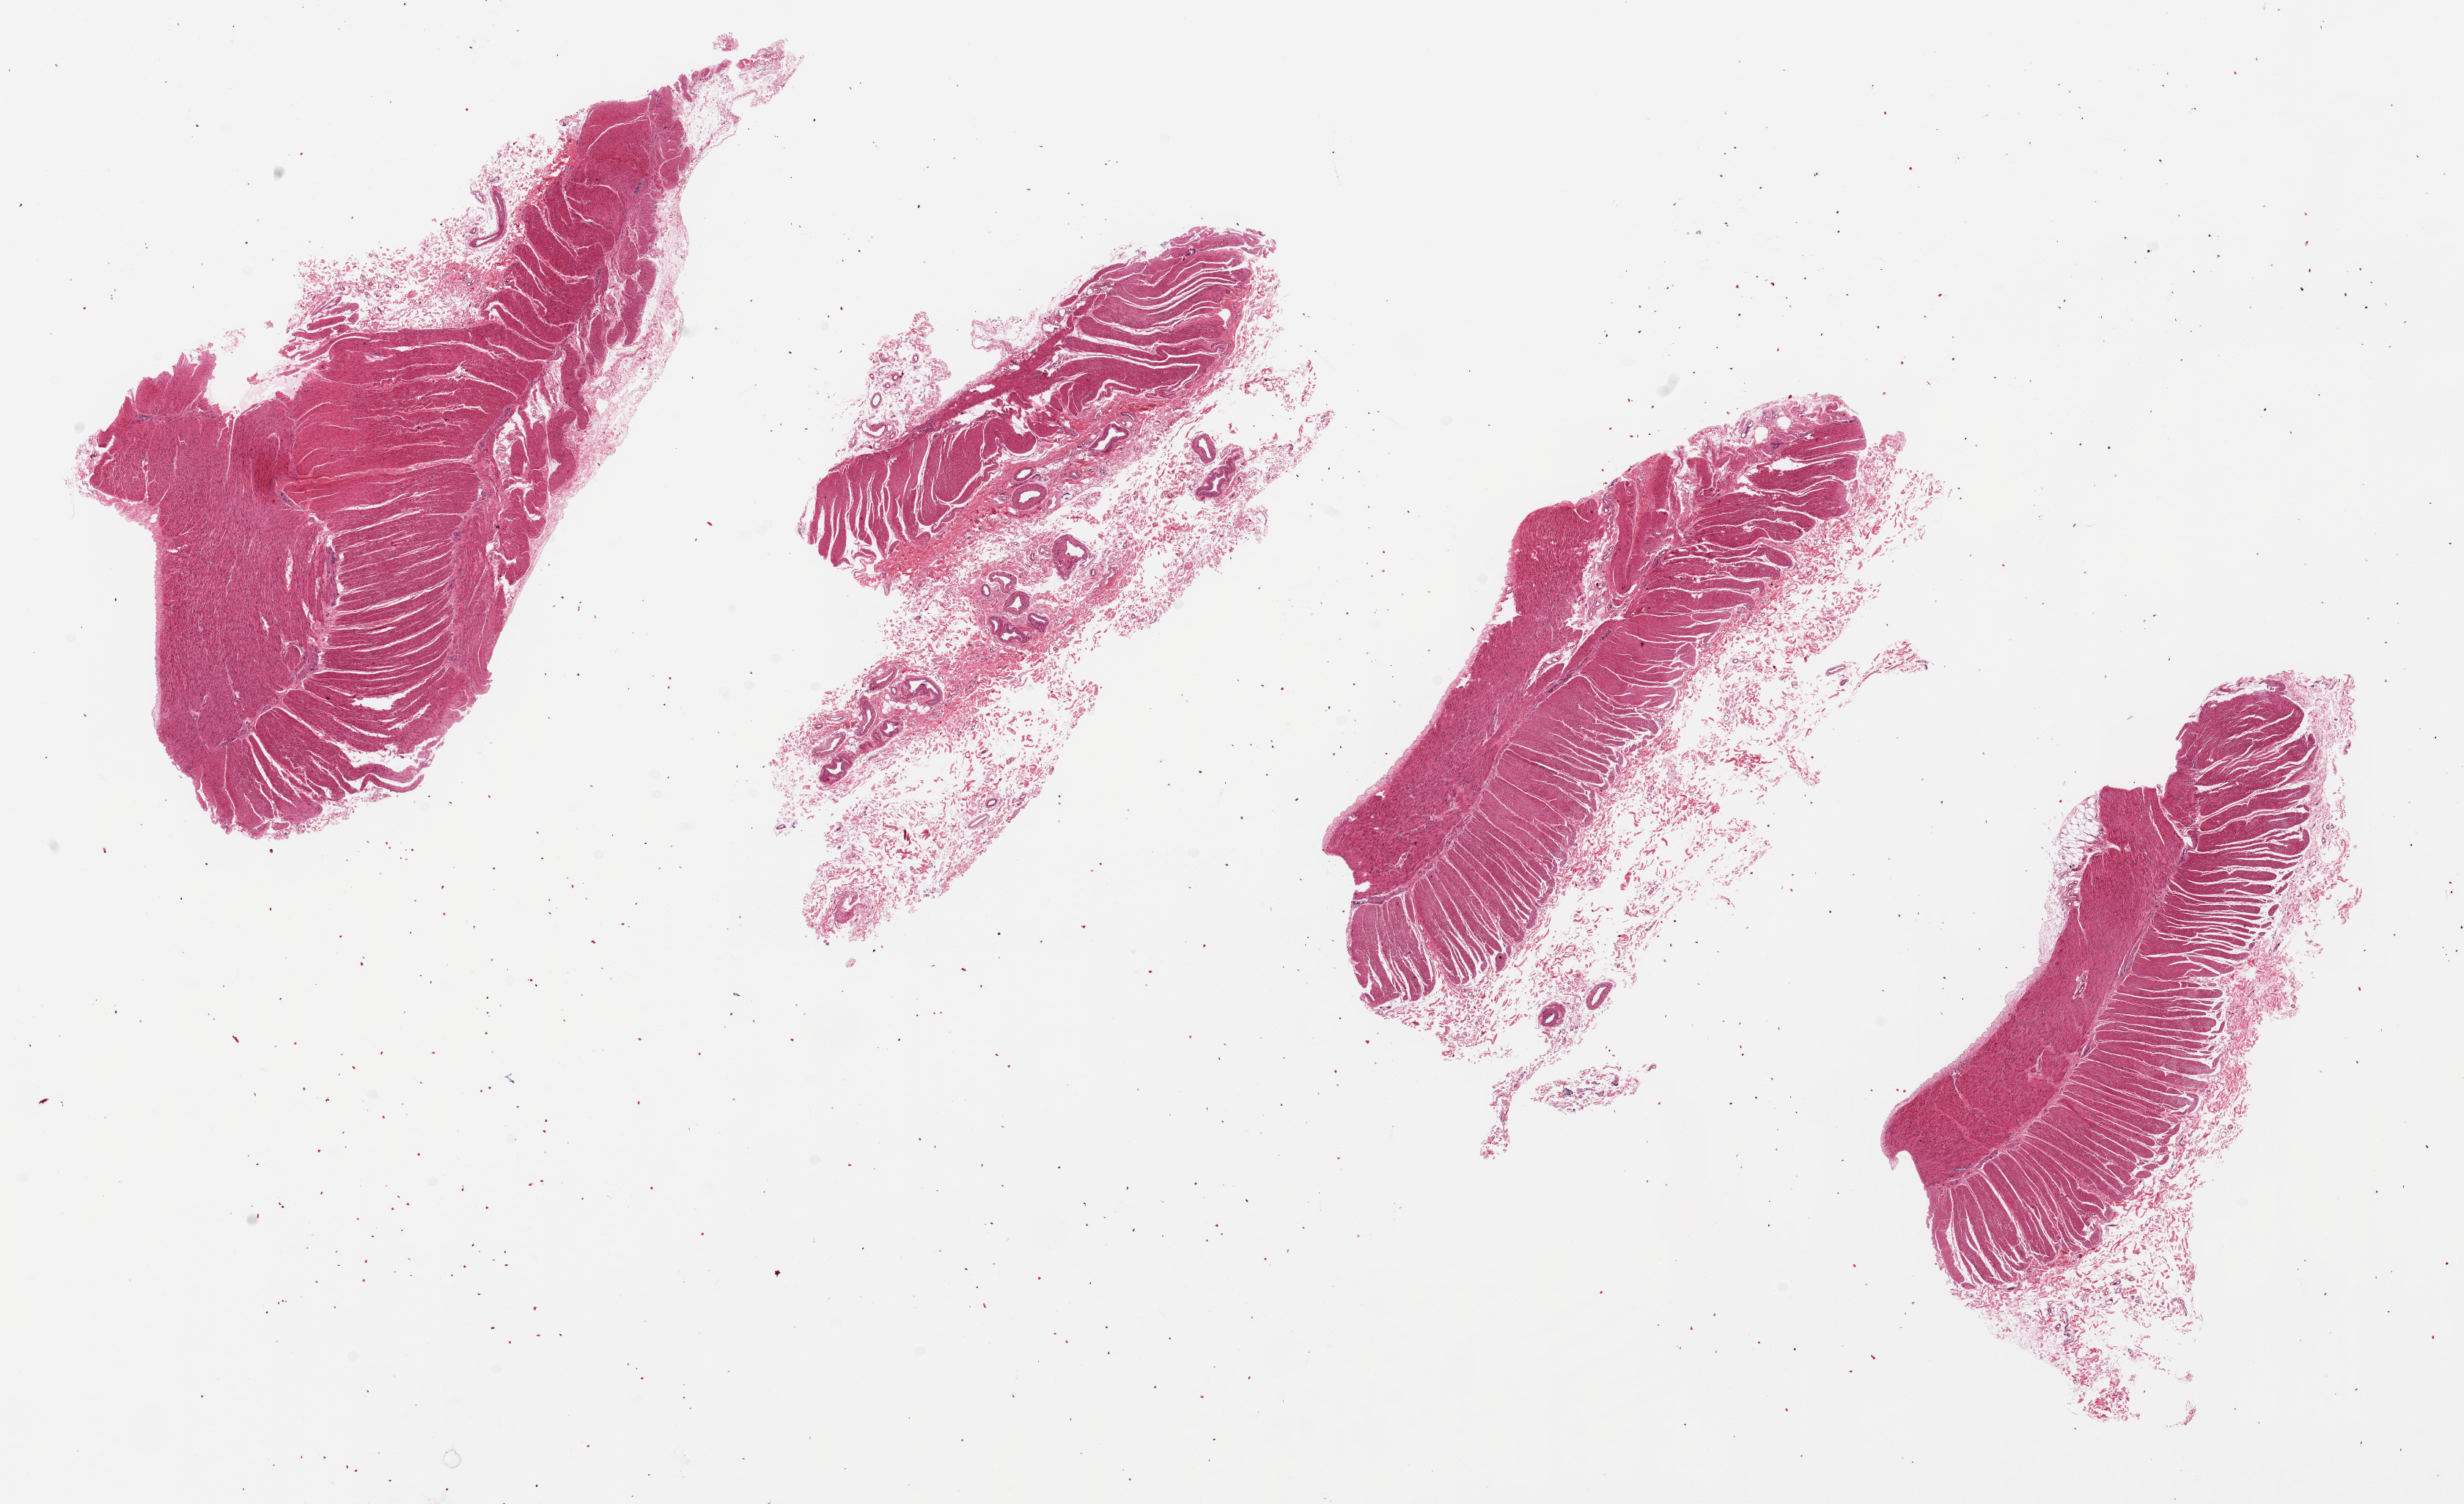
Whole-slide image, H&E stain, brightfield — shown as a low-resolution overview of the whole scanned area (about 26.6 x 16.2 mm, from a 20x scan); PAXgene-fixed, paraffin-embedded tissue; section of transverse colon (target tissue); tissue donor sample. Male donor.
Pathologist's review note for this sample: 6 pieces, none with visible mucosa.